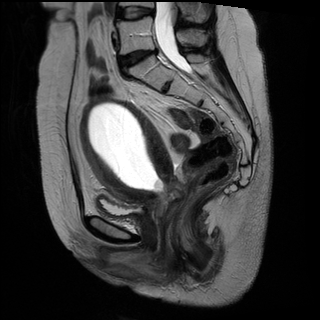
Pelvic MRI for cervical cancer, one sagittal slice; position 15 of 29 along the scan axis; T2-weighted; 1.5 T; TE 89 ms, TR 2930 ms; 4 mm slice thickness; 320 × 320 image matrix. Patient: female, 49 years.
Outlined on this slice (outlined manually by an expert reader):
- uterus and cervix: bounding box (x1, y1, x2, y2) in pixels: (79, 96, 188, 219)